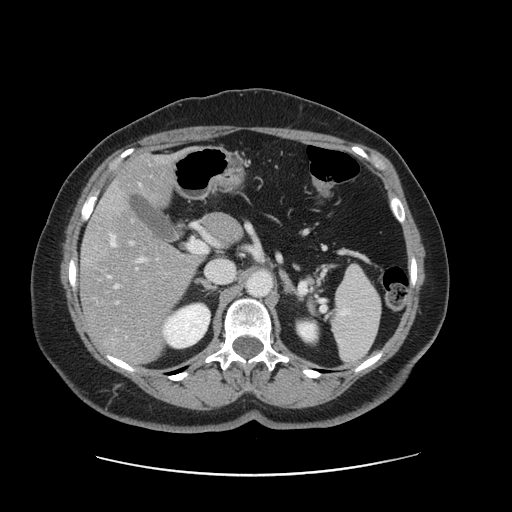
Contrast-enhanced abdominal CT, one axial slice; slice 82 of 161 in the series (ordered by position); 120 kVp; intravenous contrast given; soft-tissue window (W 400 / L 40 HU); 2.5 mm slice thickness; 512 × 512 image matrix, field of view 398 × 398 mm. Female patient, age 62 years. From the clinical record (not read from this slice): diagnosis: colorectal cancer liver metastases, imaged before liver resection; multiple liver metastases: no; largest metastasis: 2.5 cm; chemotherapy before resection: yes.
Annotated regions visible in this slice (outlined manually by an expert reader):
- hepatic veins: bounding box <108,184,142,288> (left, top, right, bottom; pixels)
- liver: <81,156,239,363>
- planned liver remnant (the part of the liver to remain after resection): <112,156,239,243>
- portal vein (with intrahepatic branches): <117,241,145,303>